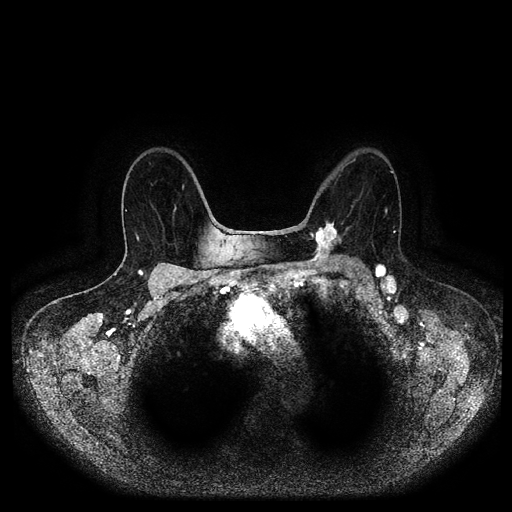
Breast MRI (dynamic contrast-enhanced, multi-phase), one axial slice; position 64 of 116 along the scan axis; dynamic contrast-enhanced series, time point 2 of 5 at this slice position (early post-contrast); 1.5 T; TE 2.6 ms, TR 5.2 ms; 2 mm slice thickness; 512 × 512 image matrix. Female patient, age 69 years.
Outlined on this slice (semi-automatically segmented with operator editing):
- breast lesion (labelled 'tumour' in the annotation; benign lesions carry a separate 'benign' label): bounding box (x1, y1, x2, y2) in pixels: (302, 220, 345, 266)